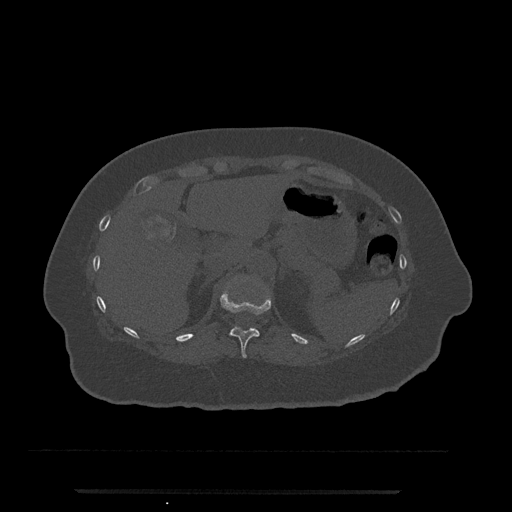
CT including the spine, one axial slice. Slice 213 of 797 in the series (ordered by position). Reconstruction kernel Br40s/3. 120 kVp. Bone window (W 1800 / L 400 HU). 0.5 mm slice thickness. 512 × 512 image matrix, field of view 440 × 440 mm. Patient: female, 51 years. Case-level facts recorded for this patient, not image findings: primary cancer: neuro.
Outlined on this slice (semi-automatic segmentation, software-assisted and operator-edited):
- T11 vertebra: bounding box (x1, y1, x2, y2) in pixels: (220, 290, 271, 358)